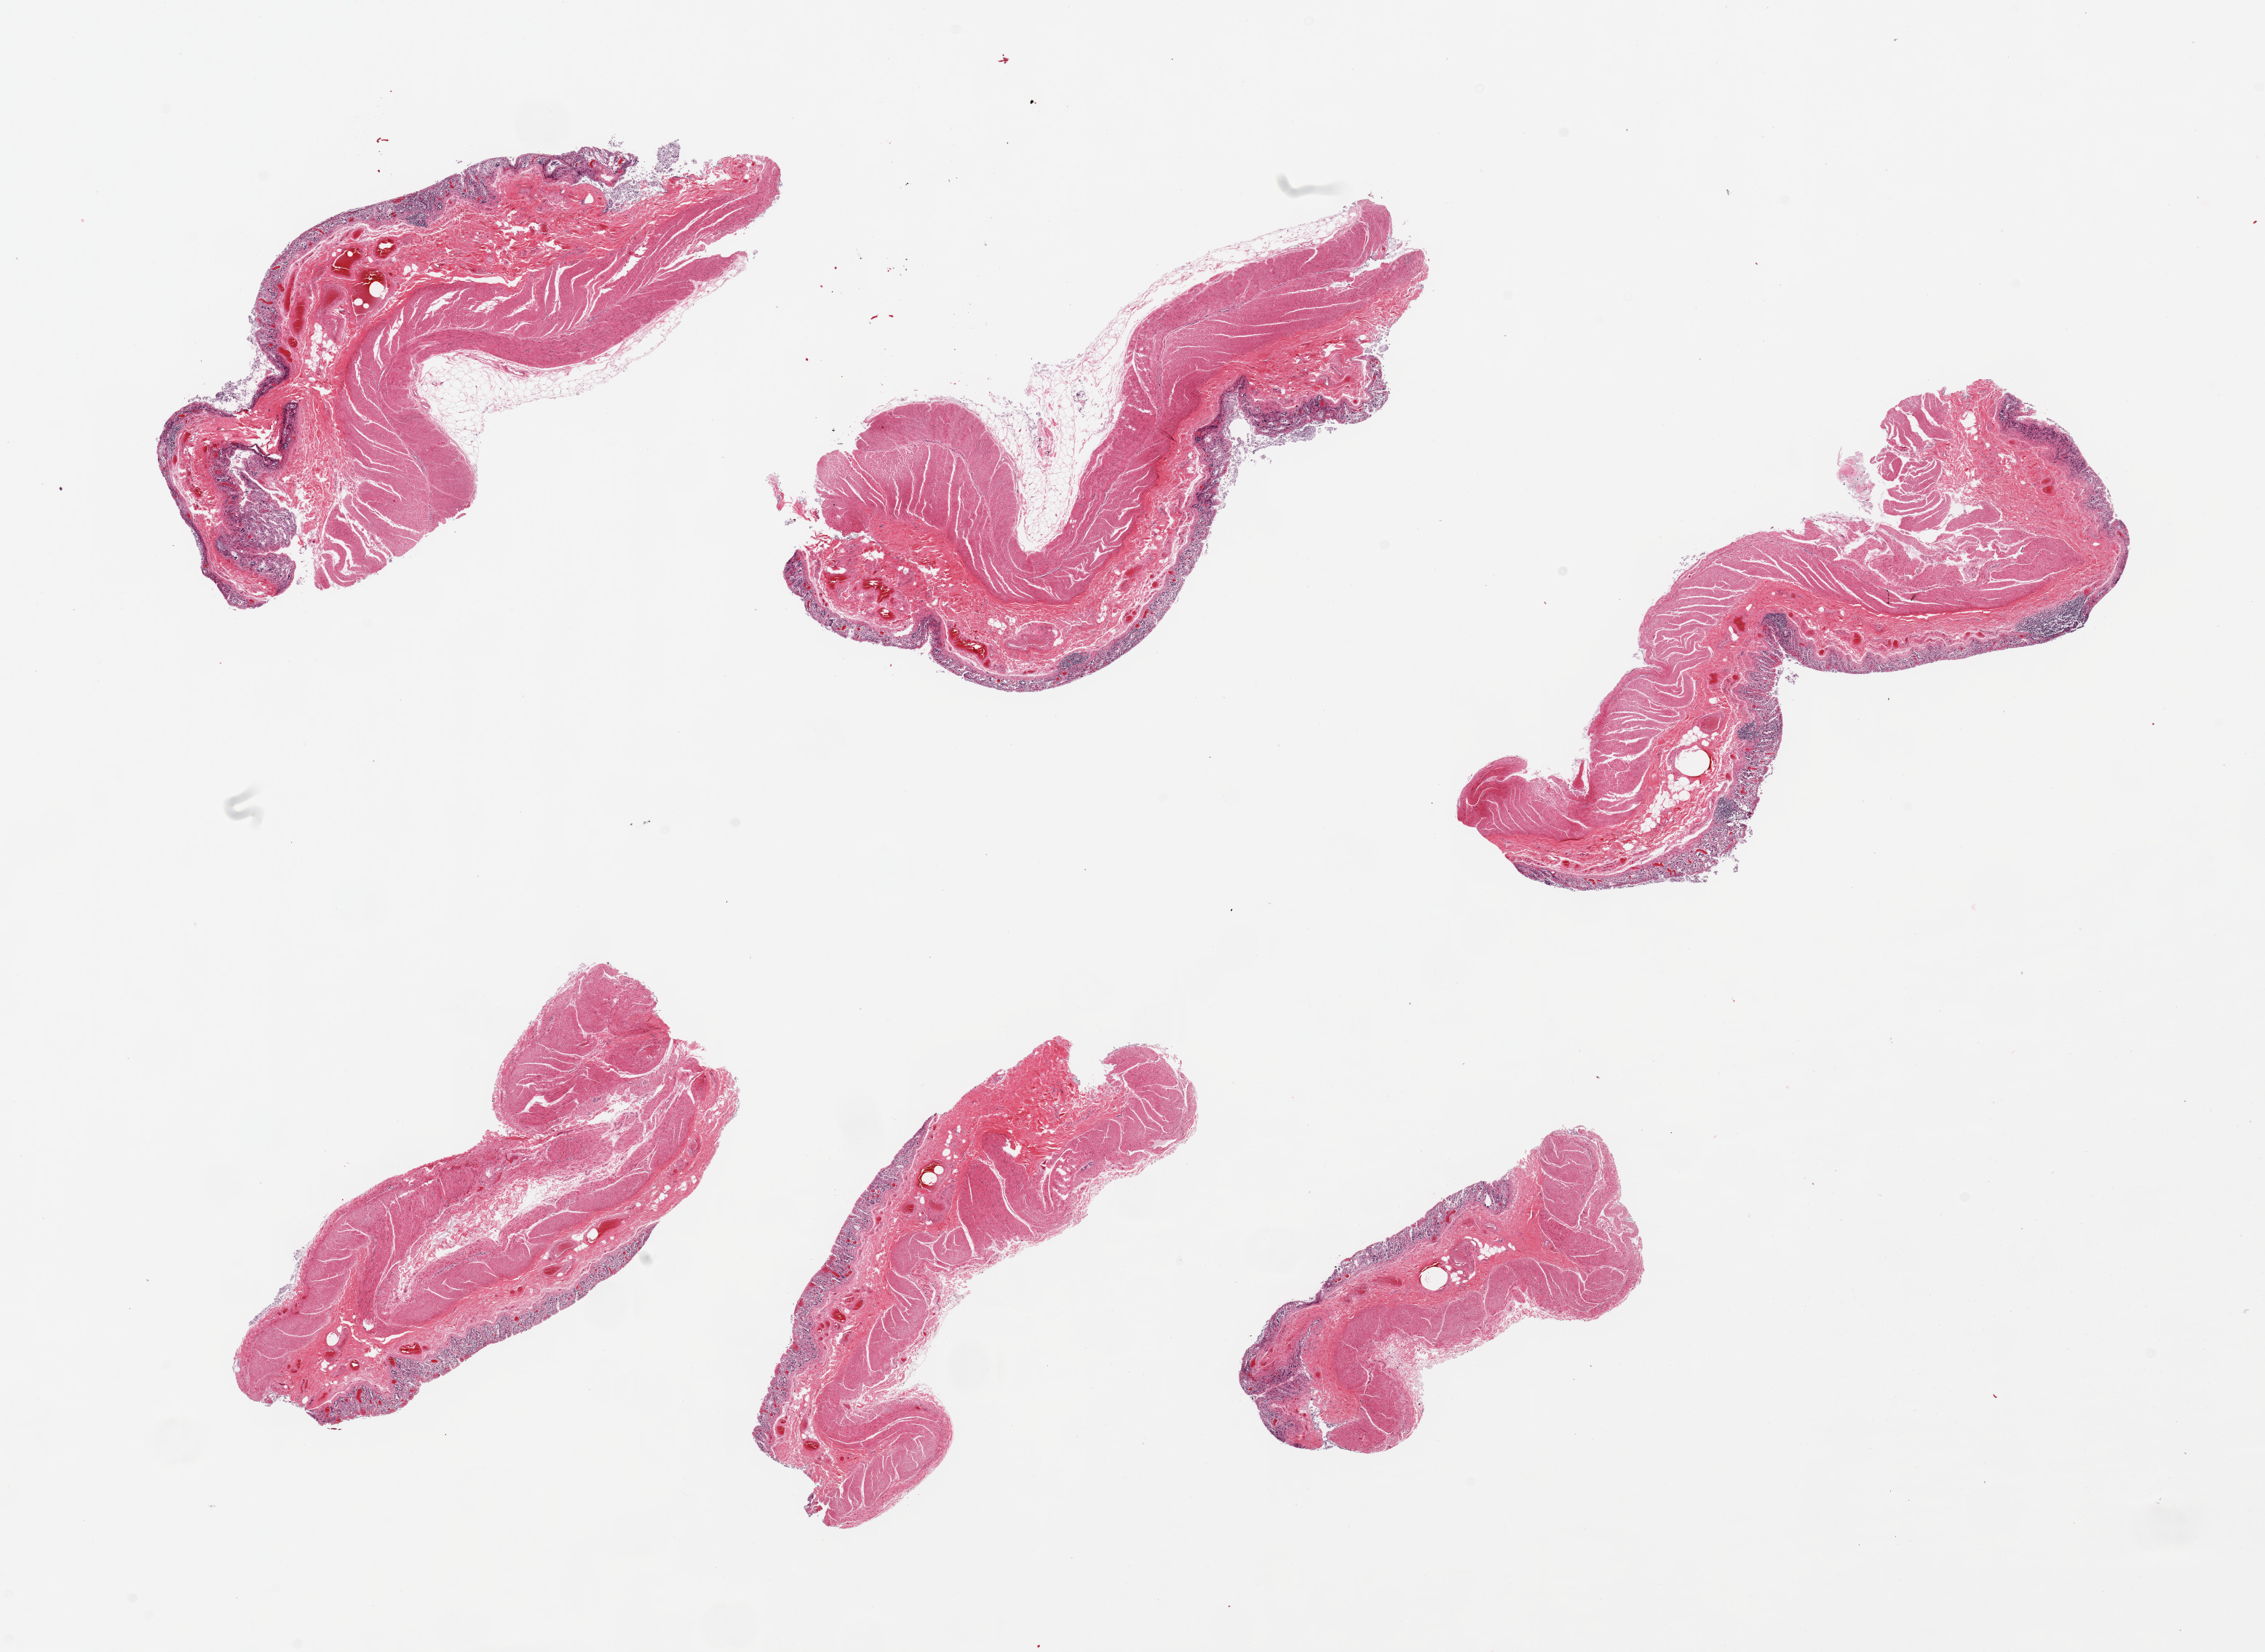
Hematoxylin and eosin (H&E) whole-slide image — low-resolution overview of the scanned area, about 24.6 x 18.0 mm (slide scanned at 20x). PAXgene-fixed paraffin-embedded (PFPE) section. Section of transverse colon (target tissue). Tissue donor sample.
Review note (as recorded): 6 pieces, mucosa totally autolyzed (glandular elements).